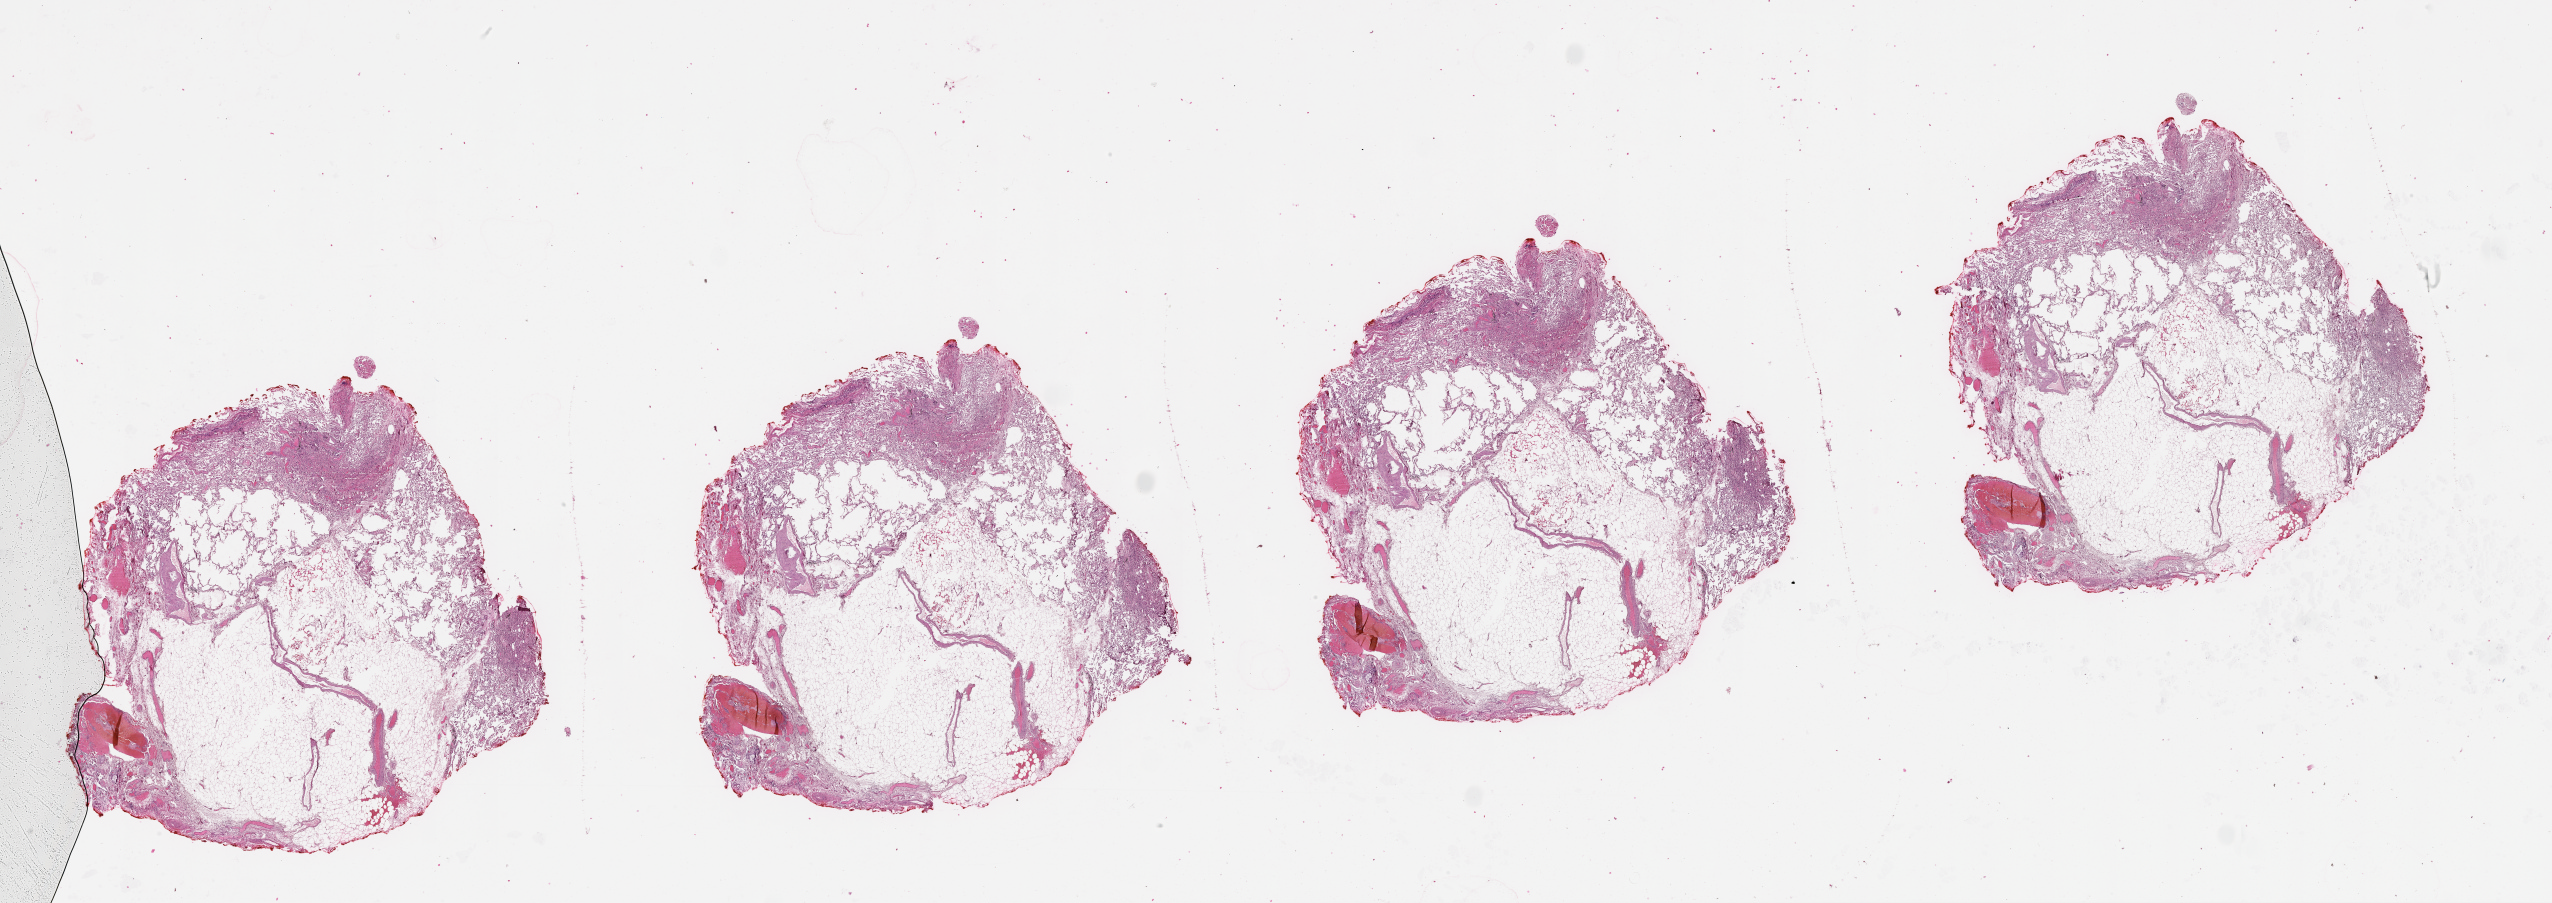
H&E-stained whole-slide image — whole scanned area (about 41.1 x 14.5 mm) shown as a low-resolution overview; lung, tissue type not recorded.
Patient diagnosis (cohort enrolment): lung adenocarcinoma (lung).